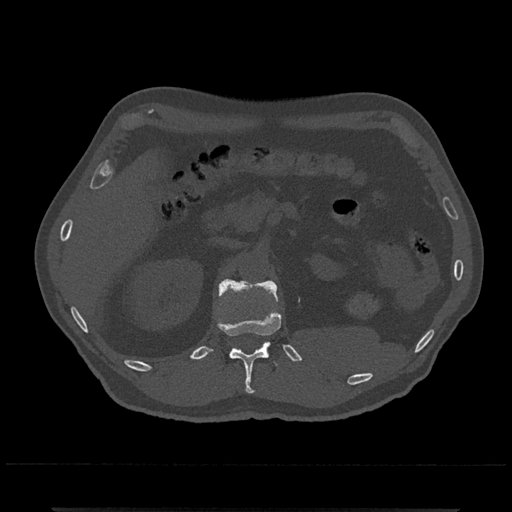
CT including the spine, one axial slice. Slice 411 of 797 in the series (ordered by position). 120 kVp. Bone window (W 1800 / L 400 HU). 0.5 mm slice thickness. 512 × 512 image matrix, field of view 393 × 393 mm. Patient: male, 67 years. From the clinical record (not read from this slice): primary cancer: prostate.
Annotated regions visible in this slice (semi-automatic segmentation, software-assisted and operator-edited):
- L1 vertebra: box from (x=219, y=279) to (x=278, y=303) px
- T12 vertebra: (x=218, y=290)–(x=282, y=394)